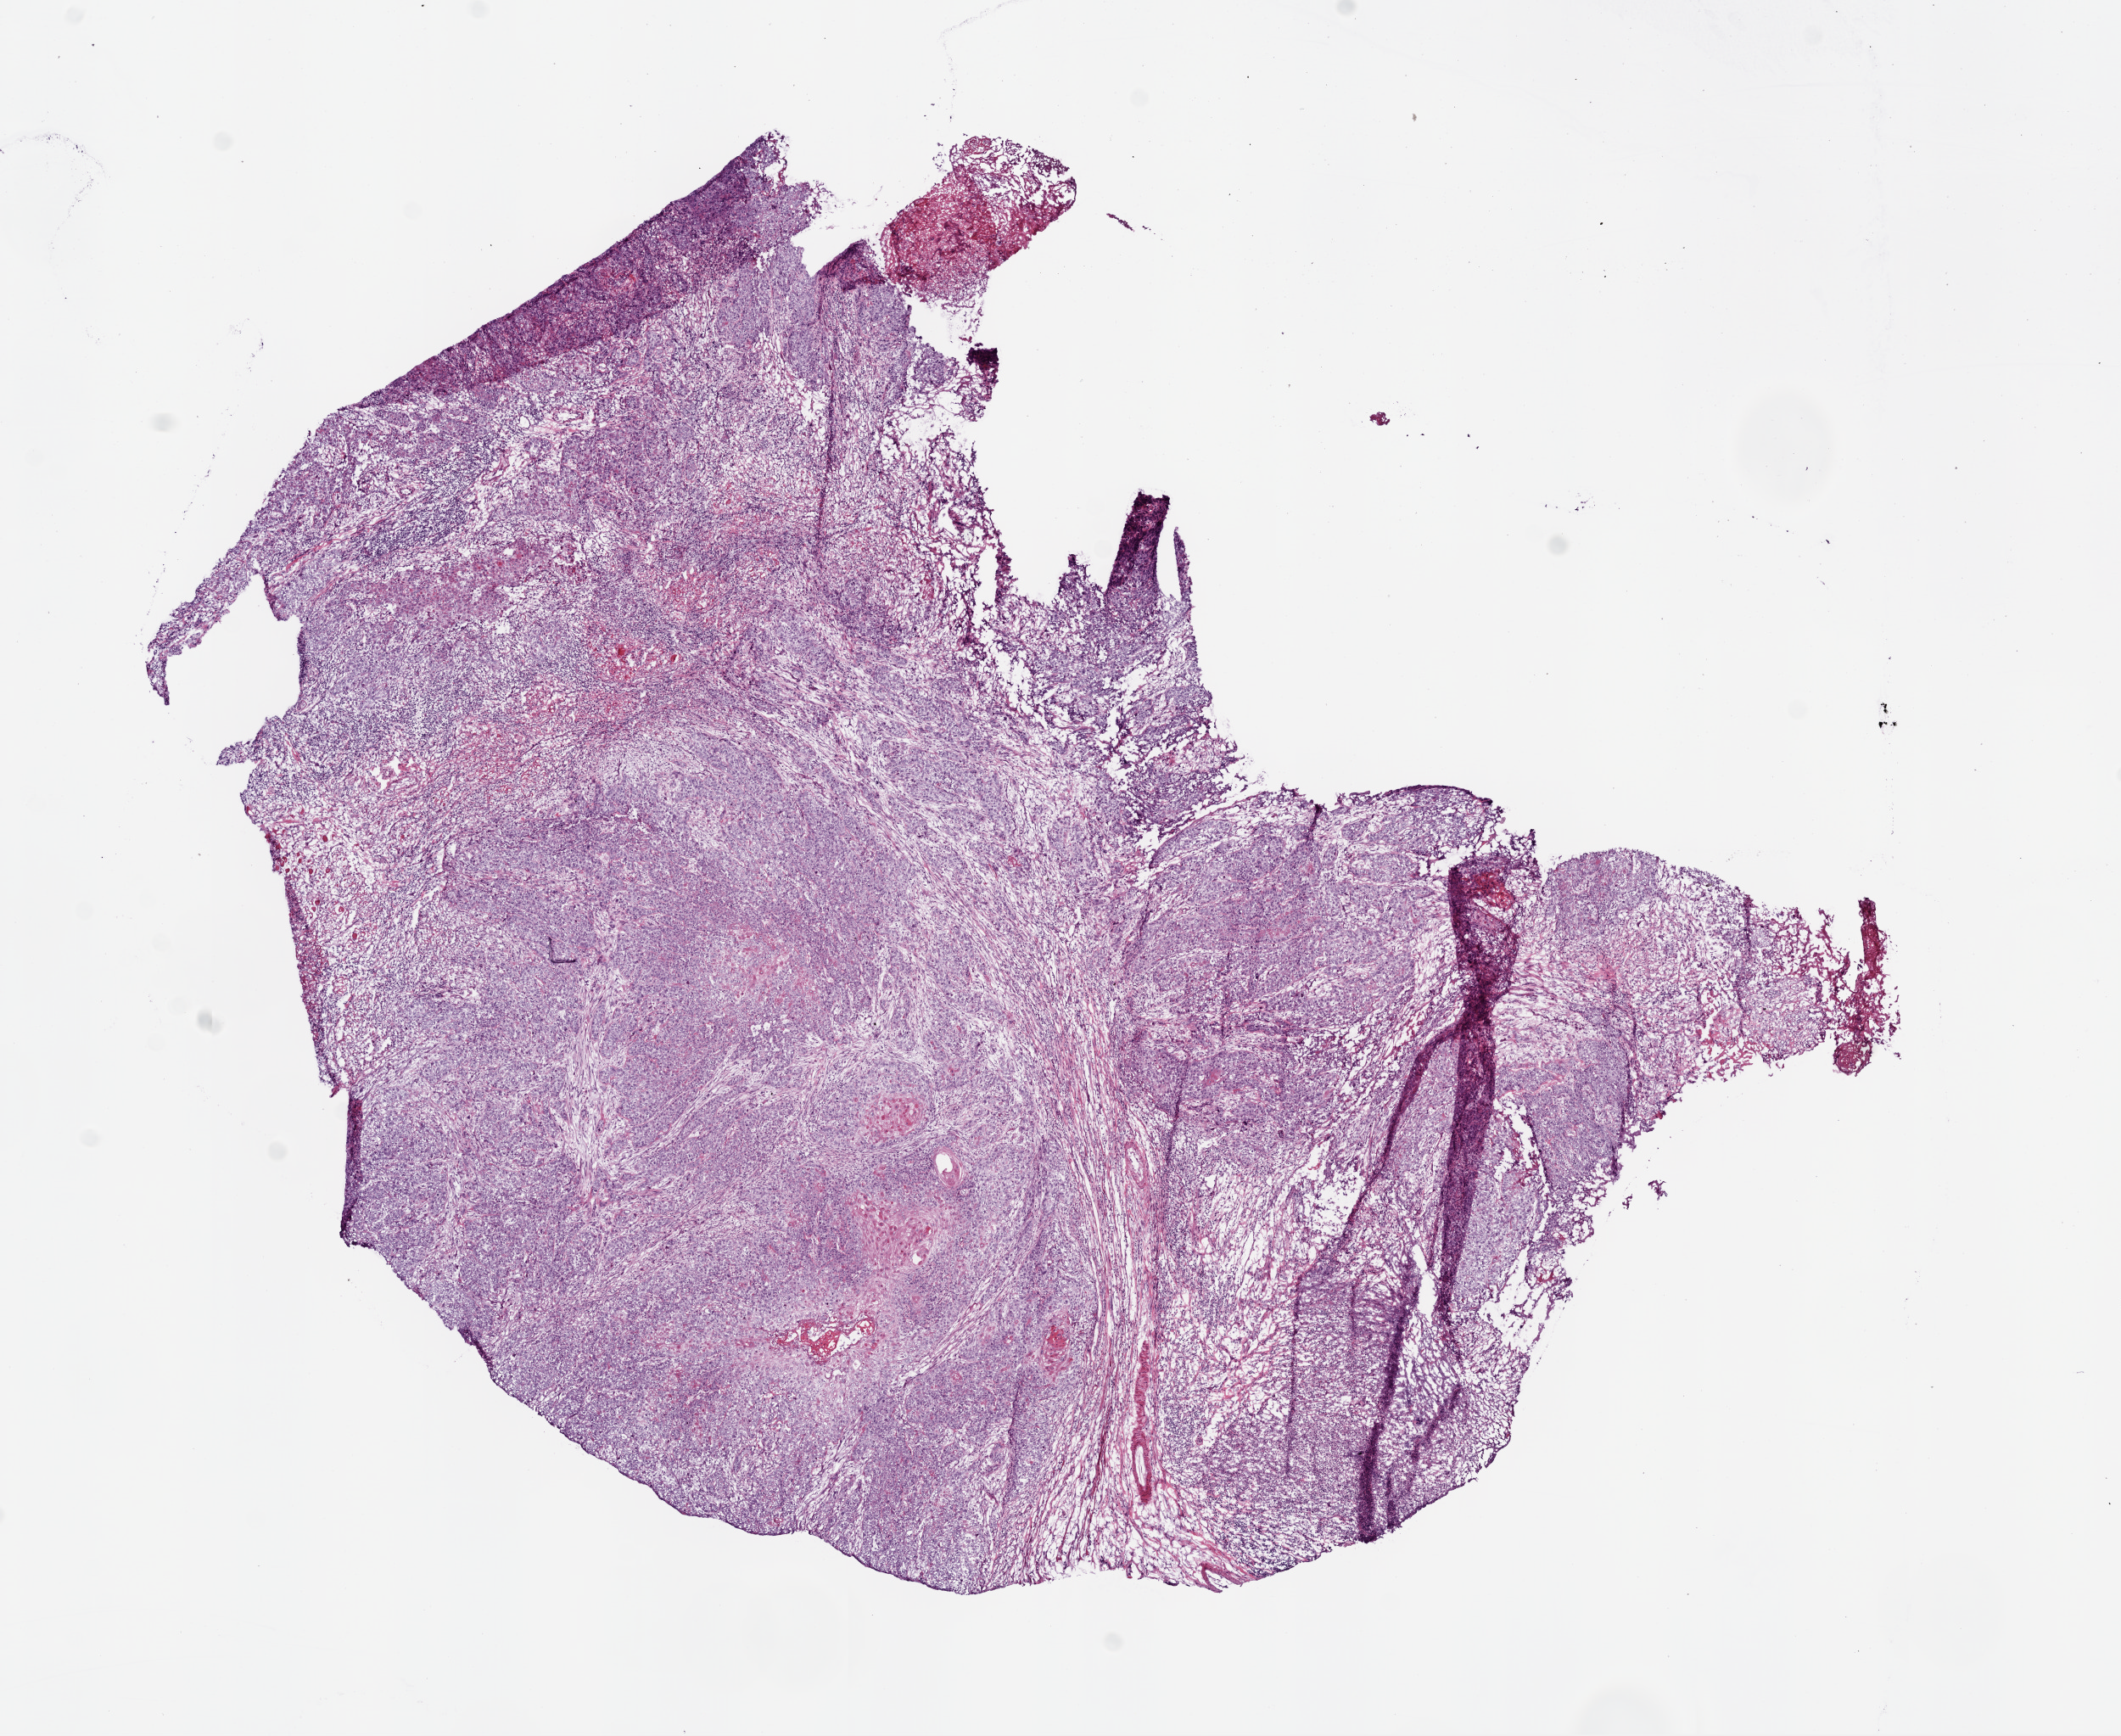
Whole-slide histology image, H&E, whole scanned area (about 10.0 x 8.2 mm, slide scanned at 20x) shown as a low-resolution overview. Frozen section from the bottom of the tissue portion. Primary tumour sample from the head and neck. Female, age 46 years at initial diagnosis. Histologic grade: G2 (moderately differentiated). Pathologist review of this section (percent, as recorded): tumour cells 90%, tumour nuclei 80%, stromal cells 9%, necrosis 1%. Infiltration values recorded for this section: lymphocyte infiltration 10%, neutrophil infiltration 1%.
Histologic diagnosis: Squamous cell carcinoma, NOS (tongue, NOS). AJCC pathologic stage: II. Laterality: left.